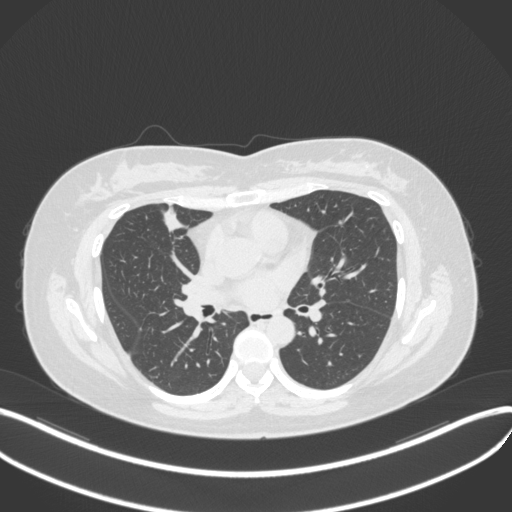
Chest CT, one axial slice. Slice 165 of 272 in the series (ordered by position). Lung window (W 1500 / L -600 HU). 1 mm slice thickness. 512 × 512 image matrix. Patient: female, 42 years. From the clinical record (not read from this slice): clinical TNM (as recorded): T1b N0 M0.
Structures marked on this image (rectangle marked by the reading radiologist):
- lung tumour (recorded histology: adenocarcinoma): box from (x=158, y=205) to (x=187, y=235) px